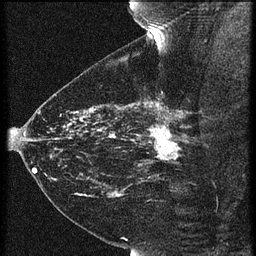
Breast MRI (dynamic contrast-enhanced), one sagittal slice; slice 43 of 60 in the series (ordered by position); 3 images stored at this slice position (order not interpretable as contrast timing); 1.5 T; TE 4.2 ms, TR 21.3 ms; 1.5 mm slice thickness; 256 × 256 image matrix, field of view 180 × 180 mm. Patient: female, 43 years. Case-level facts recorded for this patient, not image findings: setting: breast cancer imaged before/during neoadjuvant chemotherapy; receptor status: HER2-positive.
Structures marked on this image (semi-automatically segmented with operator editing):
- analysis volume of interest (the breast-tissue region the enhancement analysis was run in; not a lesion): box from (x=119, y=114) to (x=189, y=173) px
- tumour enhancement mask (voxels above the 90 % enhancement threshold inside the analysis volume of interest): (x=147, y=114)–(x=180, y=161)